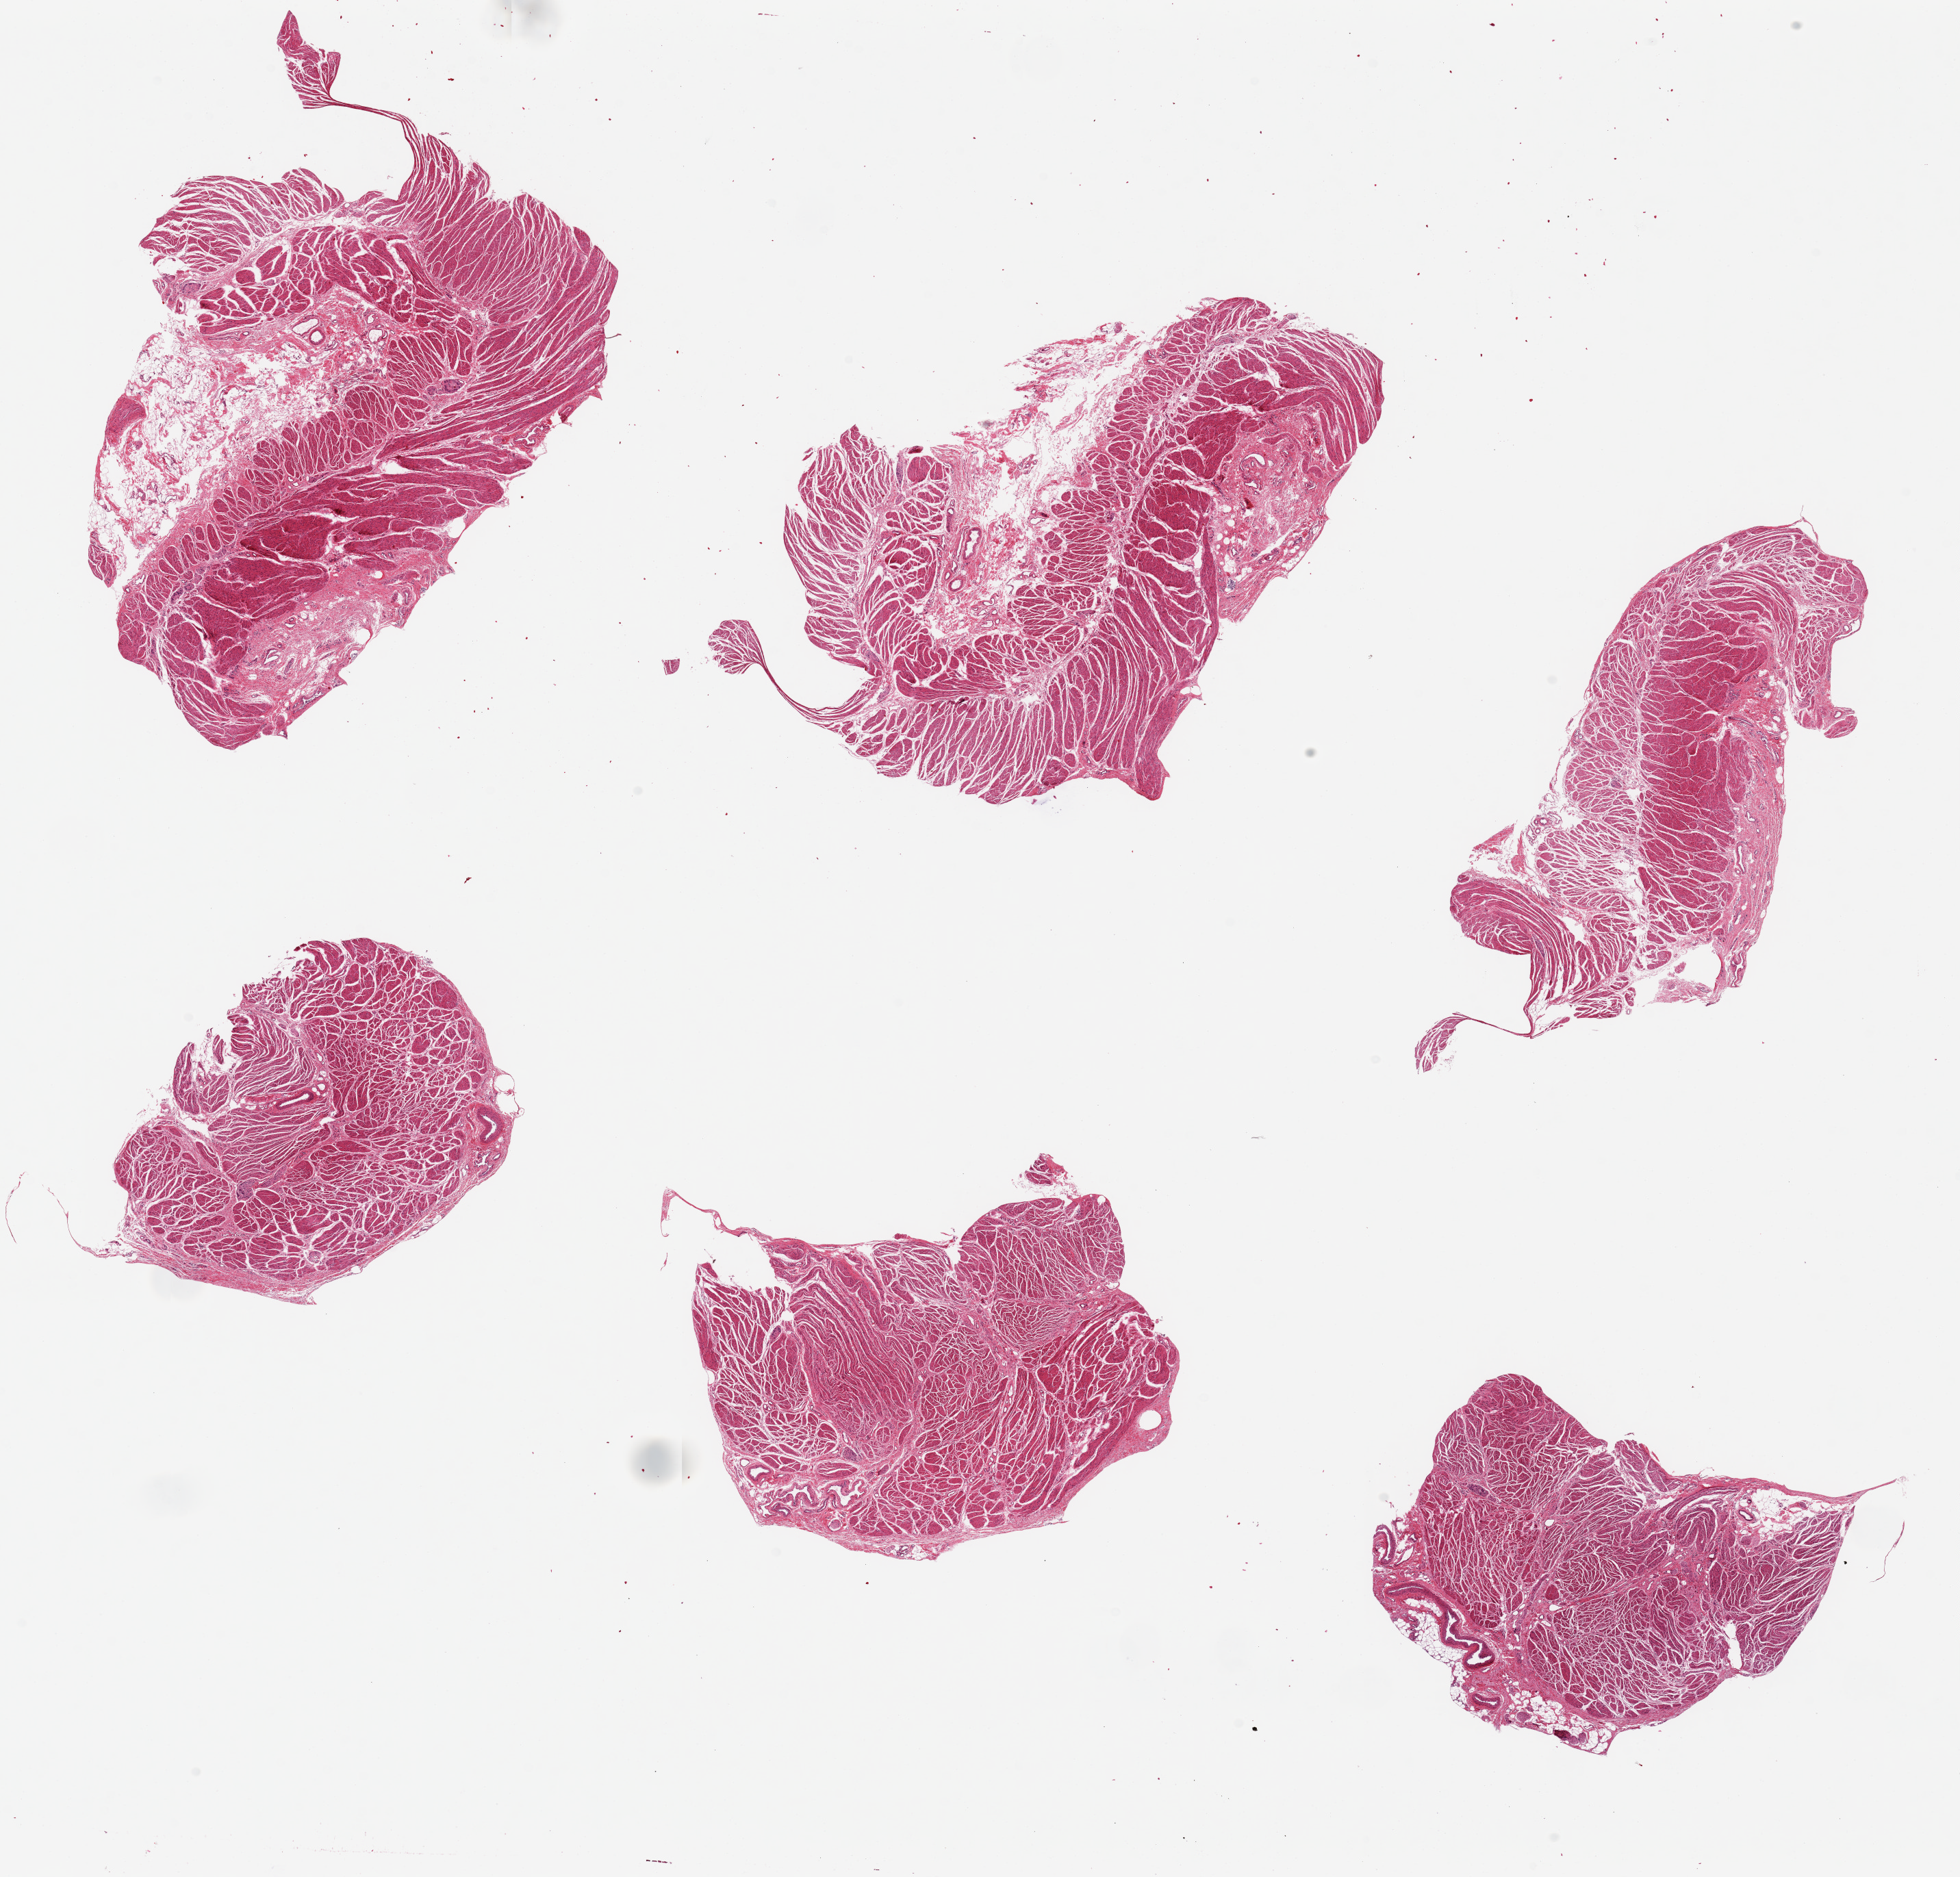
H&E whole-slide image, whole scanned area (about 22.6 x 21.7 mm) shown as a low-resolution overview. PAXgene-fixed paraffin-embedded (PFPE) section. Sampled site (target tissue): gastroesophageal junction. Donor tissue sample. Female donor.
Pathologist's review note for this sample: 6 pieces, up to 8.5x6mm; all muscle, good specimens.